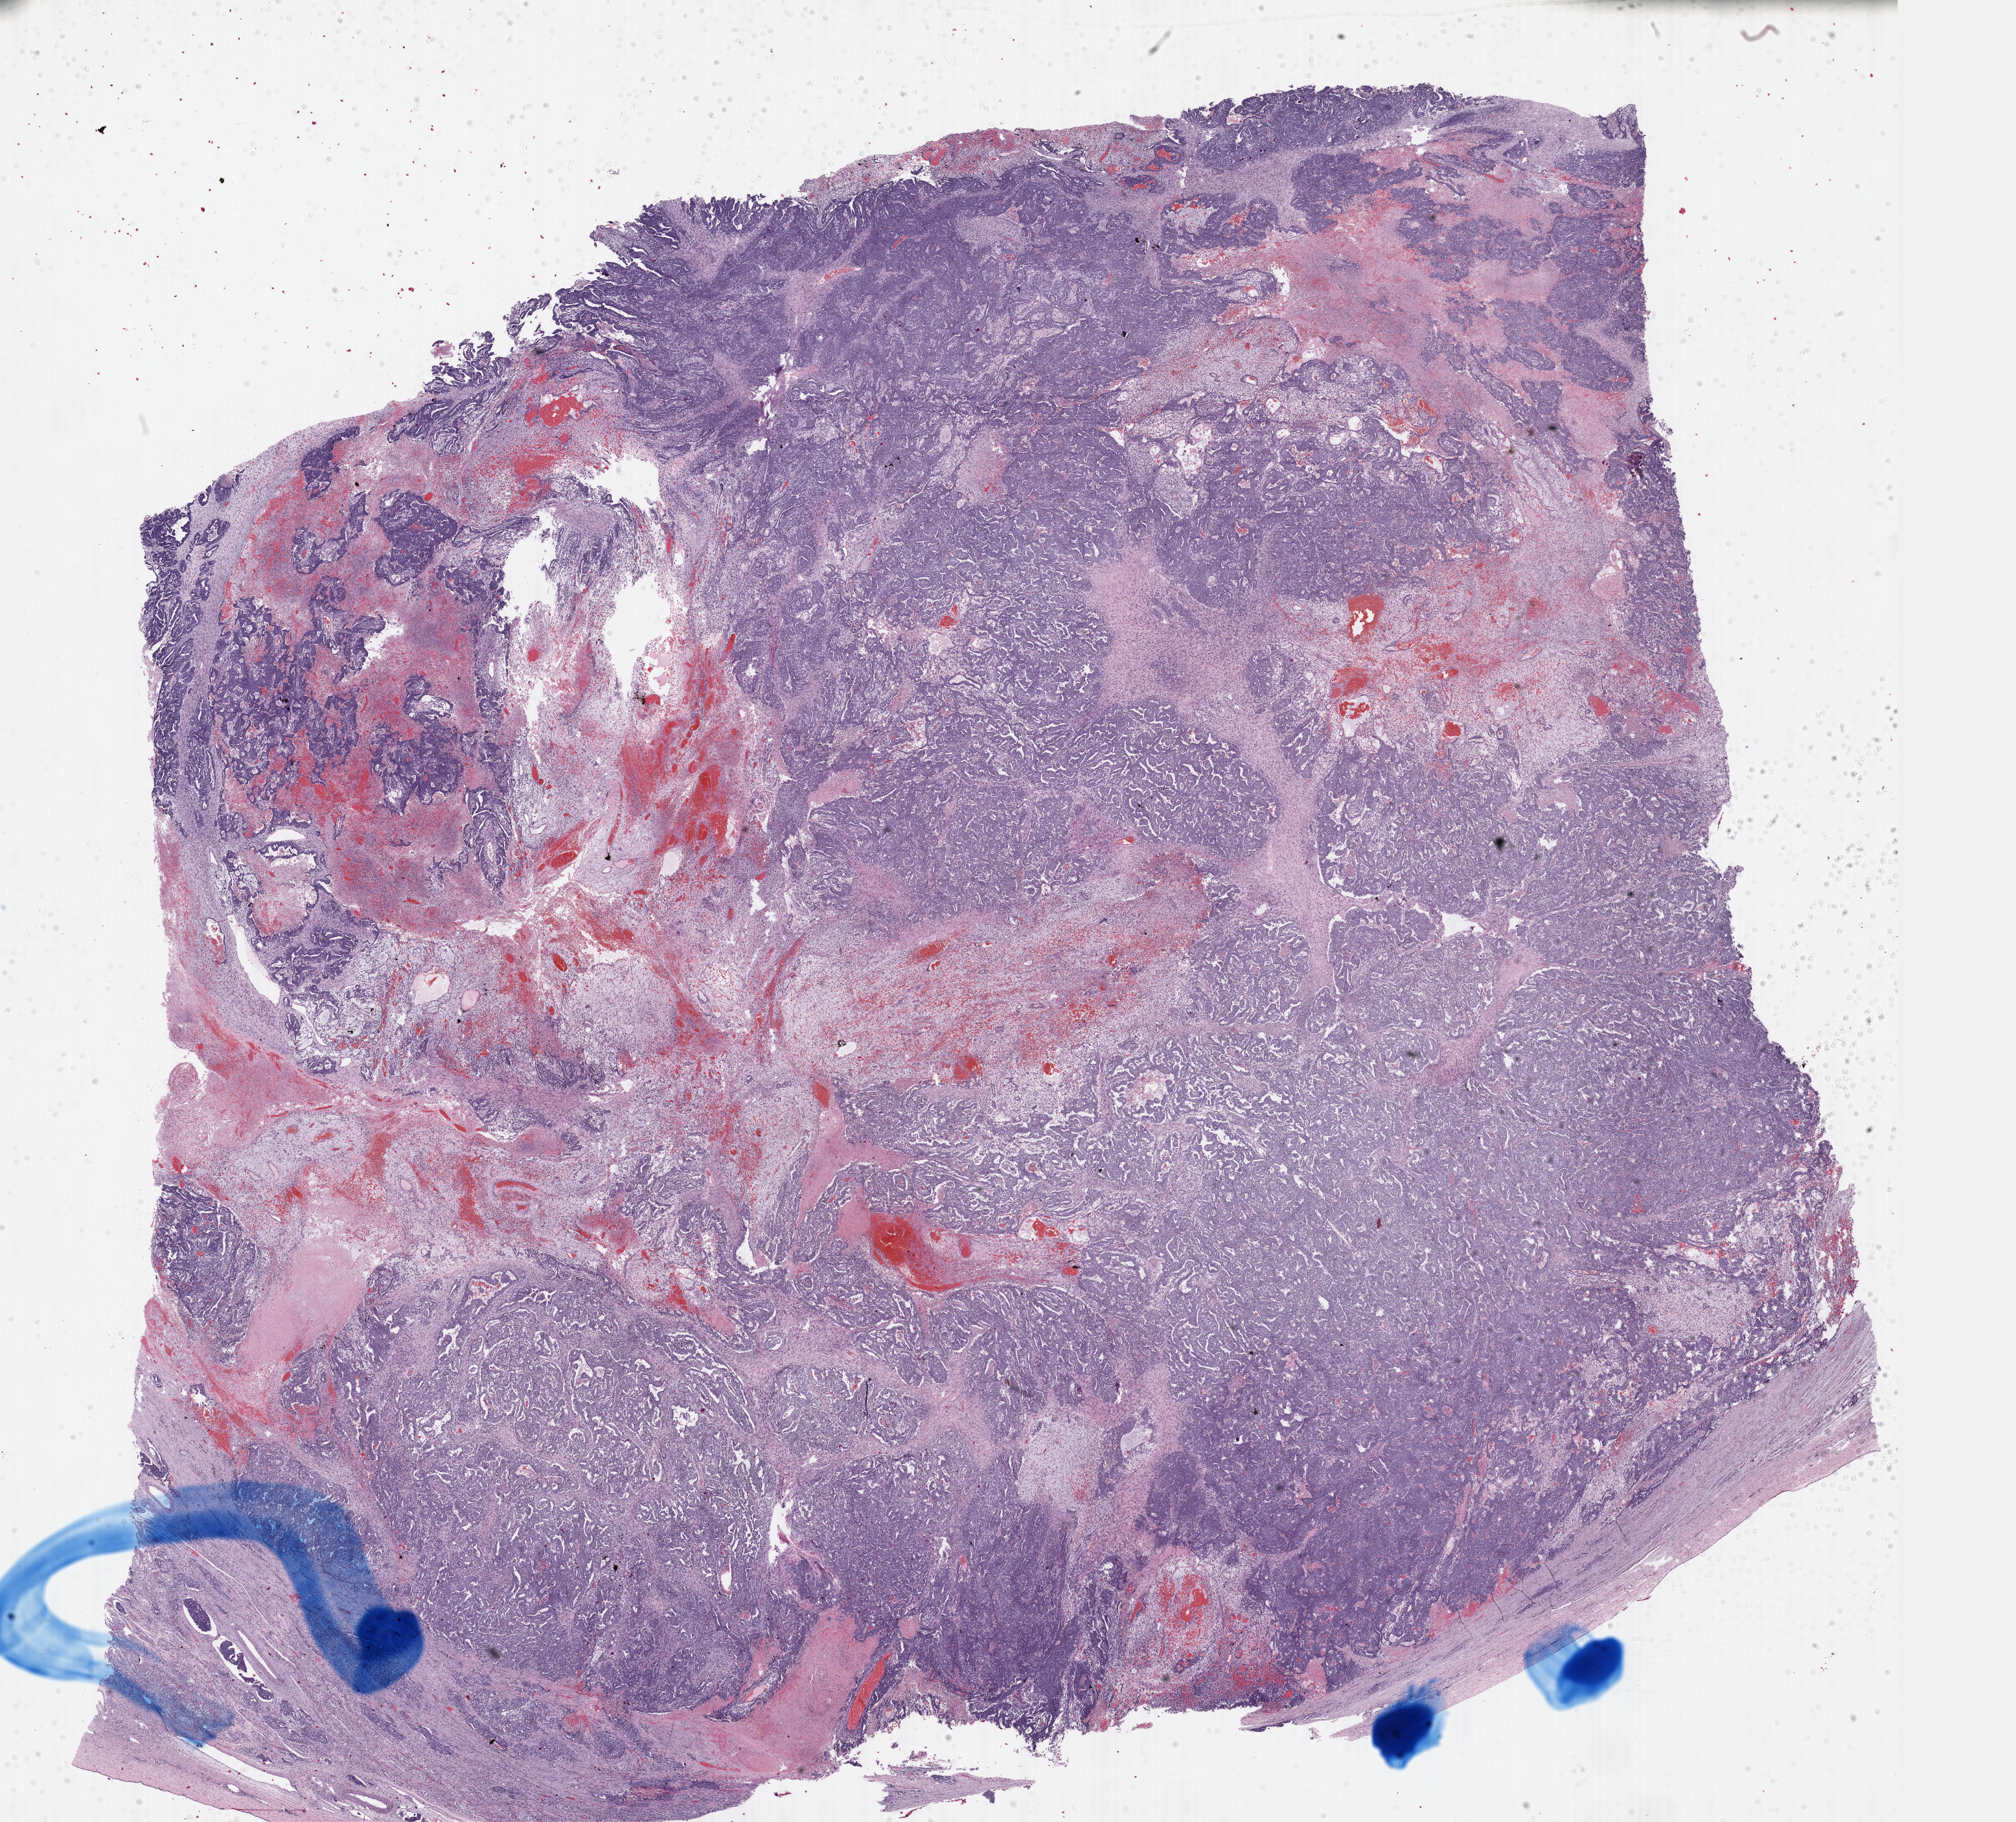
H&E whole-slide image — a low-resolution overview of the entire scanned area, about 25.1 x 22.7 mm (acquisition: 40x scan), FFPE section, sample: primary tumour, testis. Male patient; age at initial diagnosis 18 years.
- TNM: T2 NX M0
- pathologic diagnosis: Embryonal carcinoma, NOS
- laterality: right
- AJCC pathologic stage: IS (7th edition)